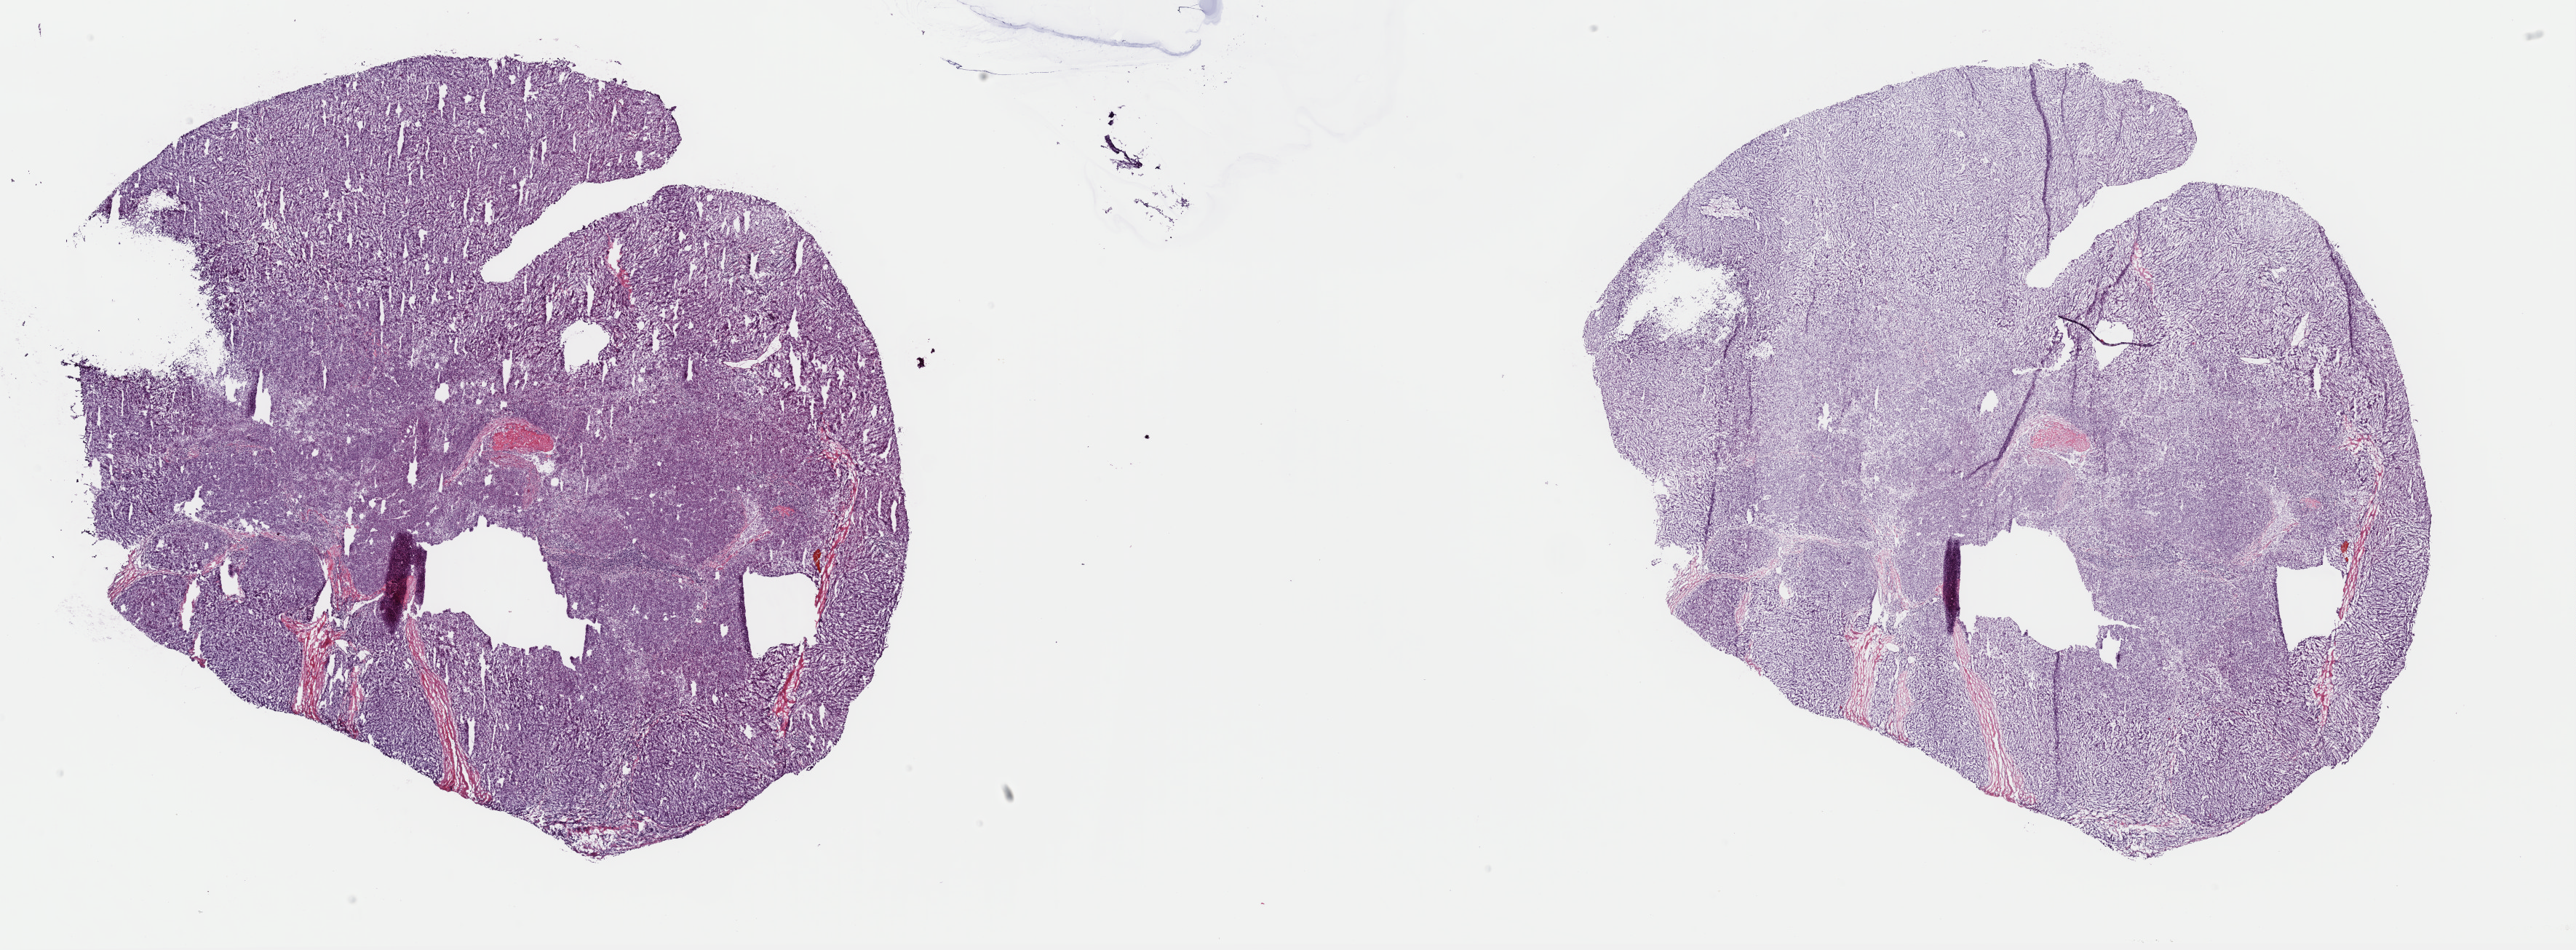
Whole-slide histology image, Hematoxylin and eosin (H&E) stained — whole scanned area (about 28.0 x 10.3 mm, slide scanned at 40x) shown as a low-resolution overview; frozen section from the top of the tissue portion; sample: primary tumour, liver. Male patient; age at initial diagnosis 73 years. Histologic grade: G2 (moderately differentiated). Composition of this section per pathologist review: tumour cells 75%, tumour nuclei 75%, normal cells 0%, stromal cells 25%, necrosis 0%. Inflammatory infiltration, as recorded: lymphocyte infiltration 6%, monocyte infiltration 1%, neutrophil infiltration 1%.
Diagnosis: Hepatocellular carcinoma, NOS. AJCC pathologic stage: IIIA.